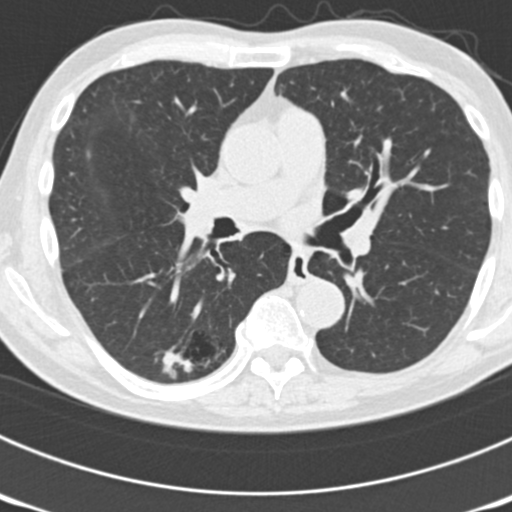
Chest CT (low-dose screening protocol), one axial image; third annual screen; lung window (W 1500 / L -600 HU); standard (soft-tissue) reconstruction kernel (B30f); 120 kVp; slice 74 of 177 in the series; 512 × 512 image matrix, field of view 300 × 300 mm. Male participant, aged 70 years at enrolment. Current smoker at enrolment.
Expert-annotated lung lesion, bounding box [x1, y1, x2, y2] px = [145, 306, 237, 385]. The screening reader recorded 3 non-calcified nodules or masses ≥4 mm on this exam; which of them this box marks is not recorded.